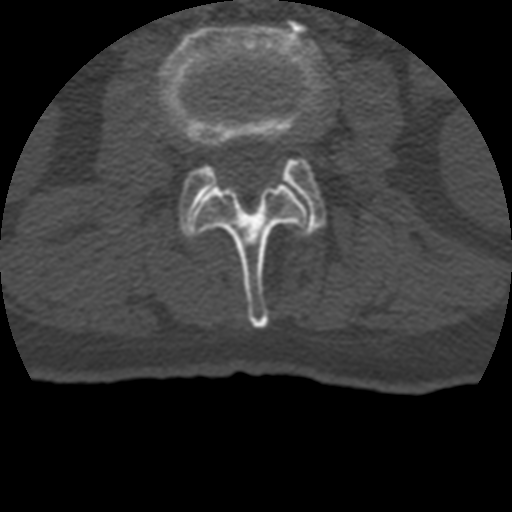
CT including the spine, one axial slice; slice 103 of 399 in the series (ordered by position); reconstruction kernel STANDARD; bone window (W 1800 / L 400 HU); 512 × 512 image matrix, field of view 160 × 160 mm. Patient age 69 years. From the clinical record (not read from this slice): primary cancer: prostate.
Structures marked on this image (semi-automatic segmentation, software-assisted and operator-edited):
- L2 vertebra: bounding box (x1, y1, x2, y2) in pixels: (194, 184, 308, 328)
- L3 vertebra: (158, 20, 329, 233)